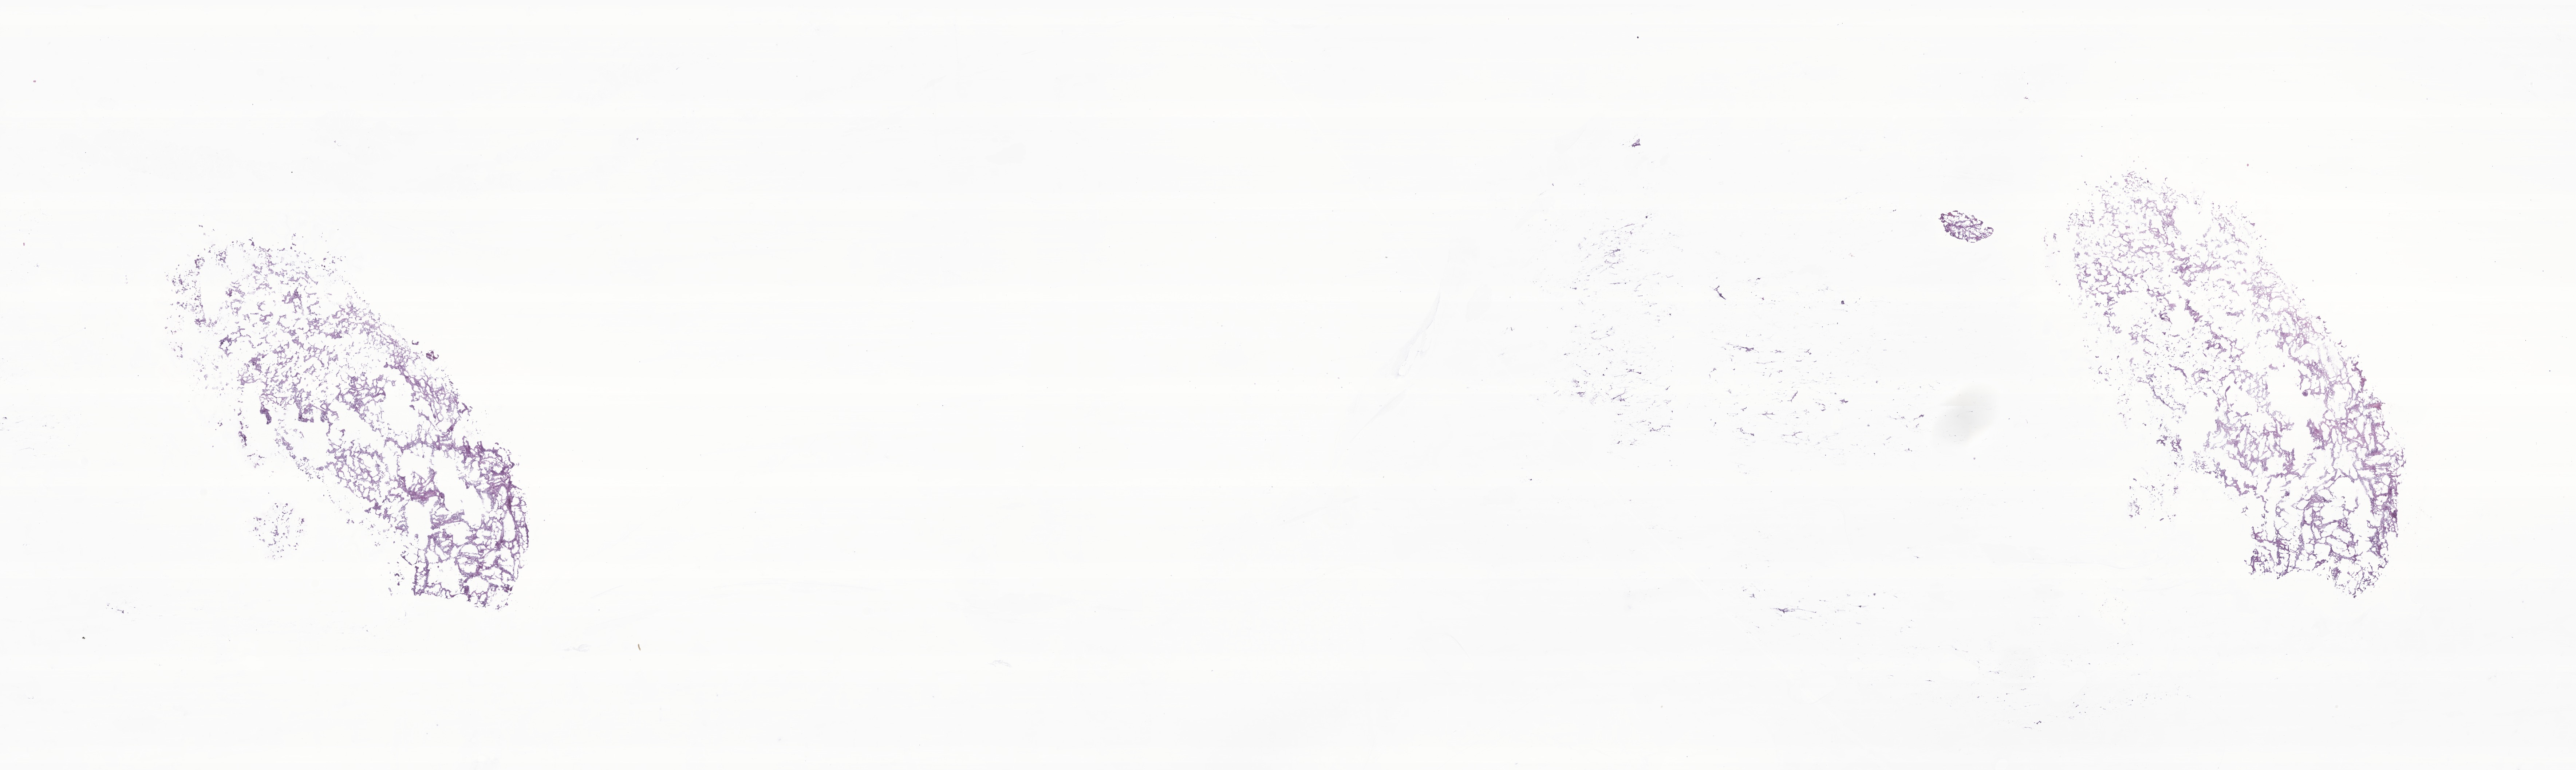
Digitized H&E-stained section of tumor tissue from the brain, a low-resolution overview of the entire scanned area, about 29.8 x 8.9 mm, frozen section. Patient: male, age 124 months (10 years 4 months).
Diagnosis (ICD-O-3 morphology term): Pilocytic astrocytoma.